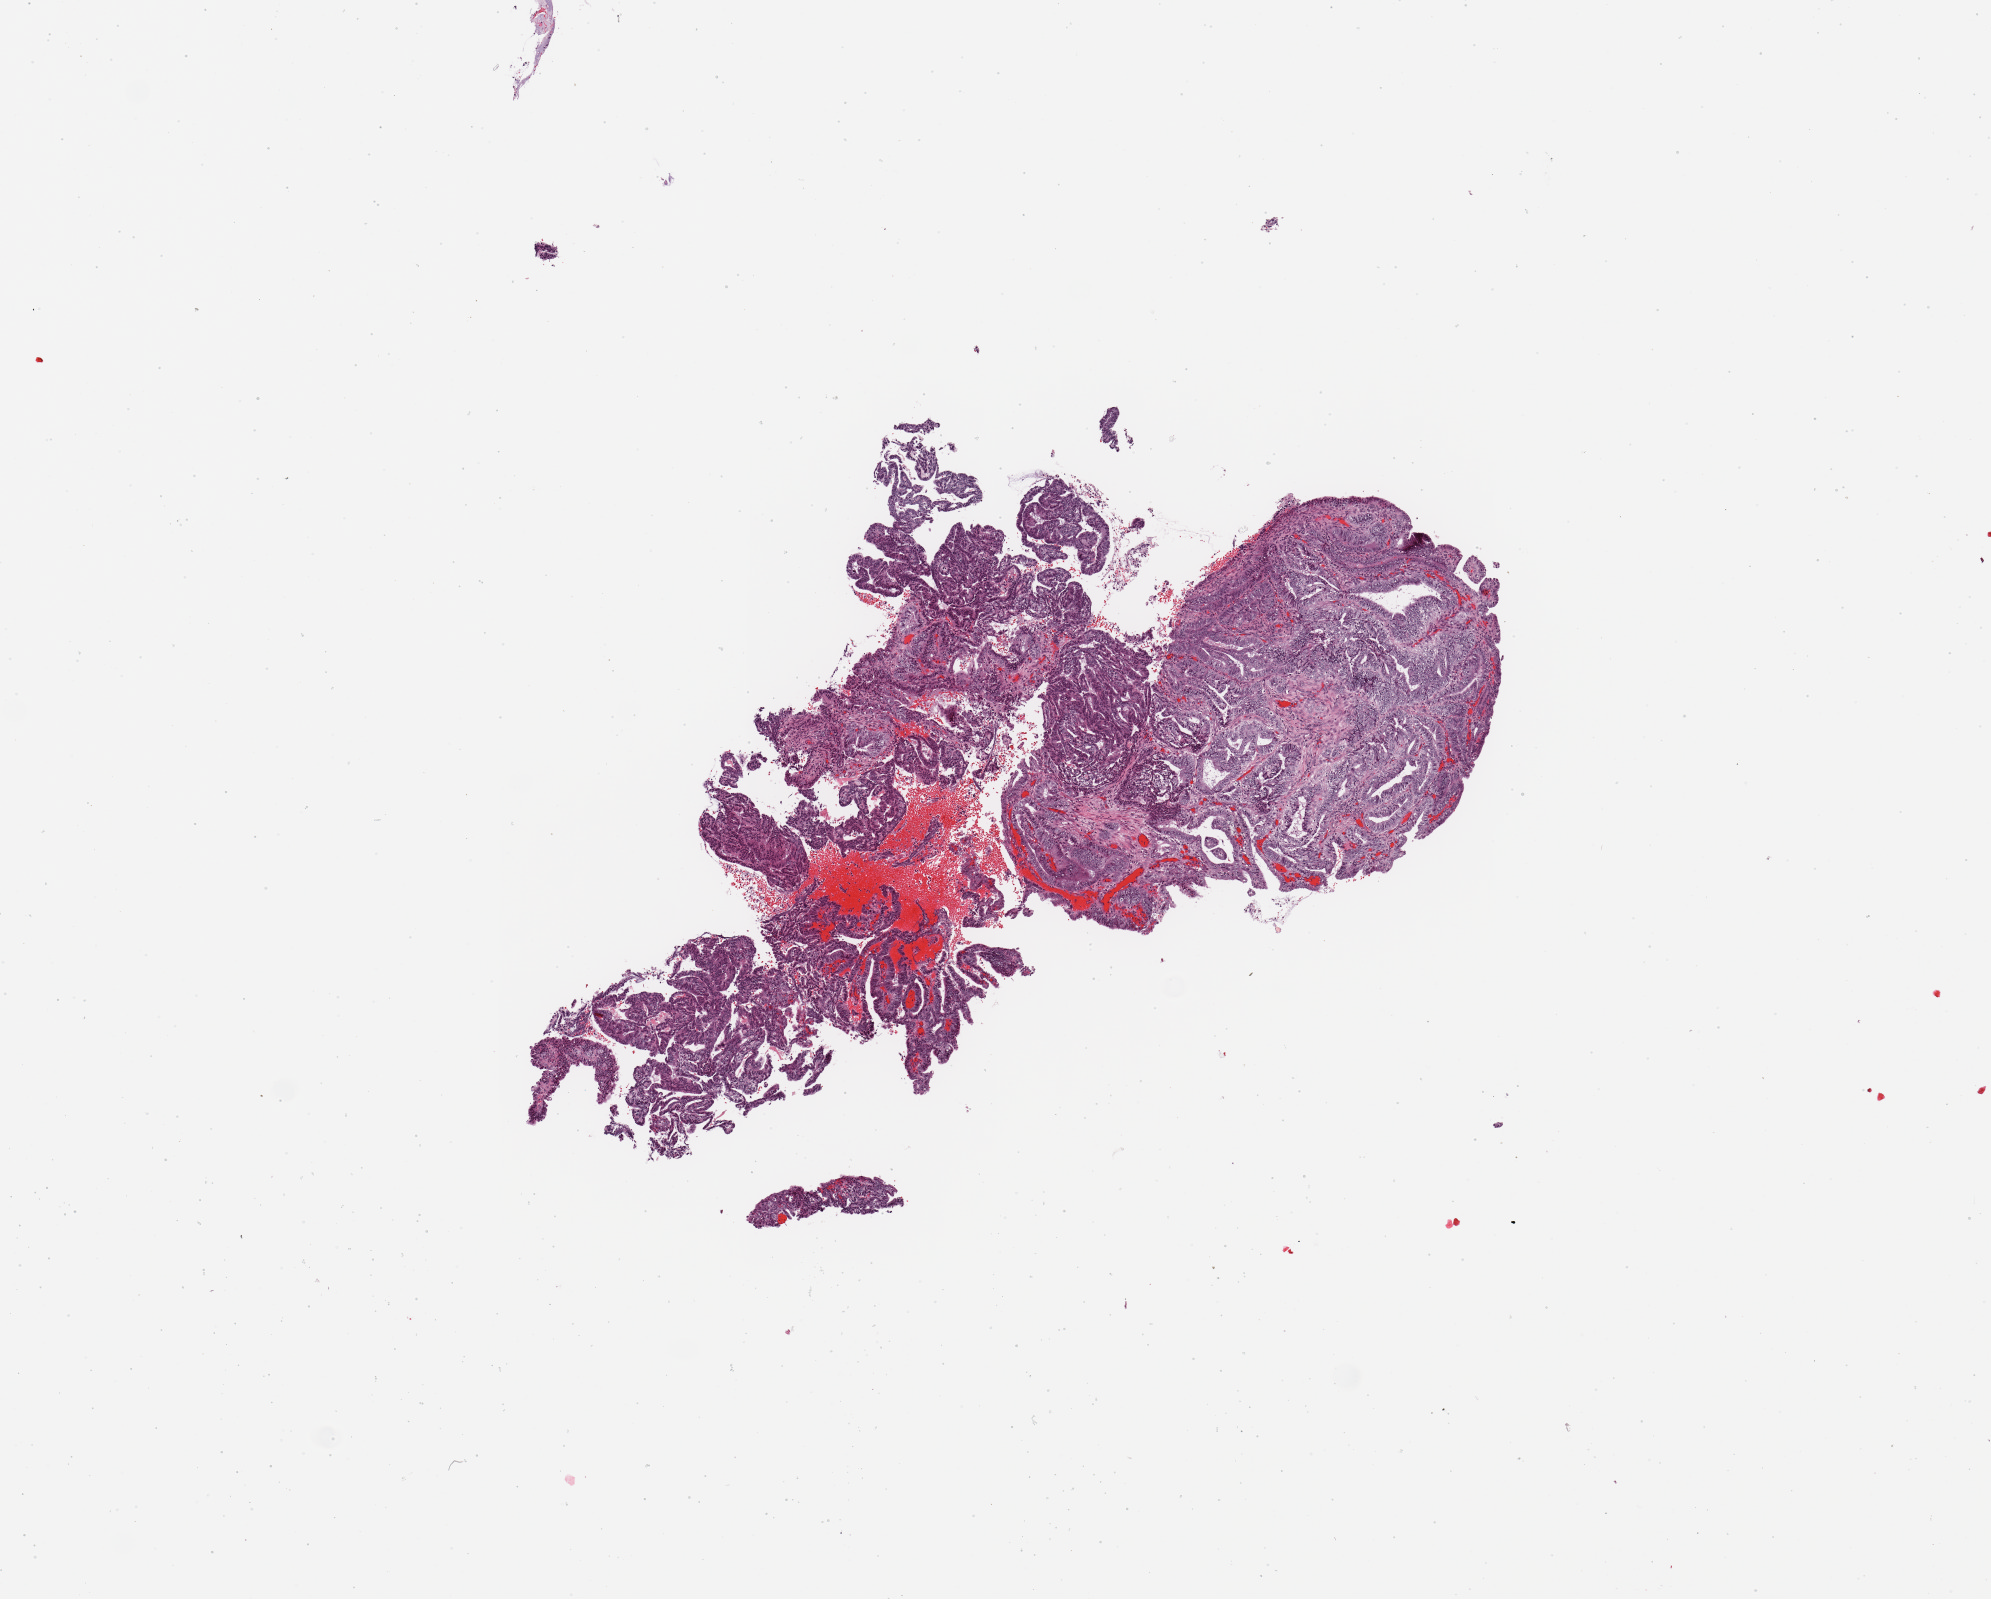
Hematoxylin and eosin (H&E) stained whole-slide image, low-resolution overview of the scanned area, about 7.9 x 6.3 mm, tumour tissue sample, sampled site: uterus. Patient: female, age 71 years. Slide review estimates, as recorded: tumour nuclei 90%, necrosis 0%.
Diagnosis: Endometrioid adenocarcinoma, NOS.